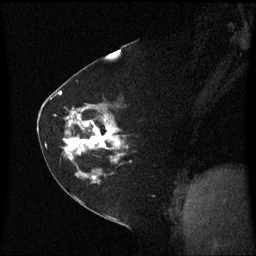
Breast MRI (dynamic contrast-enhanced), one sagittal slice; slice 36 of 60 in the series (ordered by position); dynamic contrast-enhanced series, image 2 of 3 at this slice position (ordered by acquisition); 1.5 T; TE 4.2 ms, TR 8.4 ms; 2 mm slice thickness; 256 × 256 image matrix. Female patient, age 60 years. Case-level facts recorded for this patient, not image findings: setting: breast cancer imaged before/during neoadjuvant chemotherapy; receptor status: triple-negative.
Annotated regions visible in this slice (semi-automatic segmentation, software-assisted and operator-edited):
- analysis volume of interest (the breast-tissue region the enhancement analysis was run in; not a lesion): bounding box <45,99,133,182> (left, top, right, bottom; pixels)
- tumour enhancement mask (voxels above the 70 % enhancement threshold inside the analysis volume of interest): <64,108,126,181>